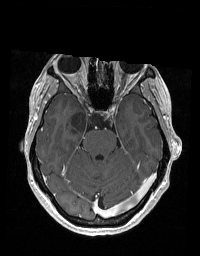
Brain MRI from a brain-tumour surgery series, one axial slice; T1-weighted post-contrast; 1 mm slice thickness; 200 × 256 image matrix. Case-level facts recorded for this patient, not image findings: histopathology: Glioblastoma; WHO grade: 2; IDH mutation: no; tumour location: Right Skull Base Temporal.
Outlined on this slice (manually delineated by an expert):
- tumour: bounding box <72,112,101,134> (left, top, right, bottom; pixels)